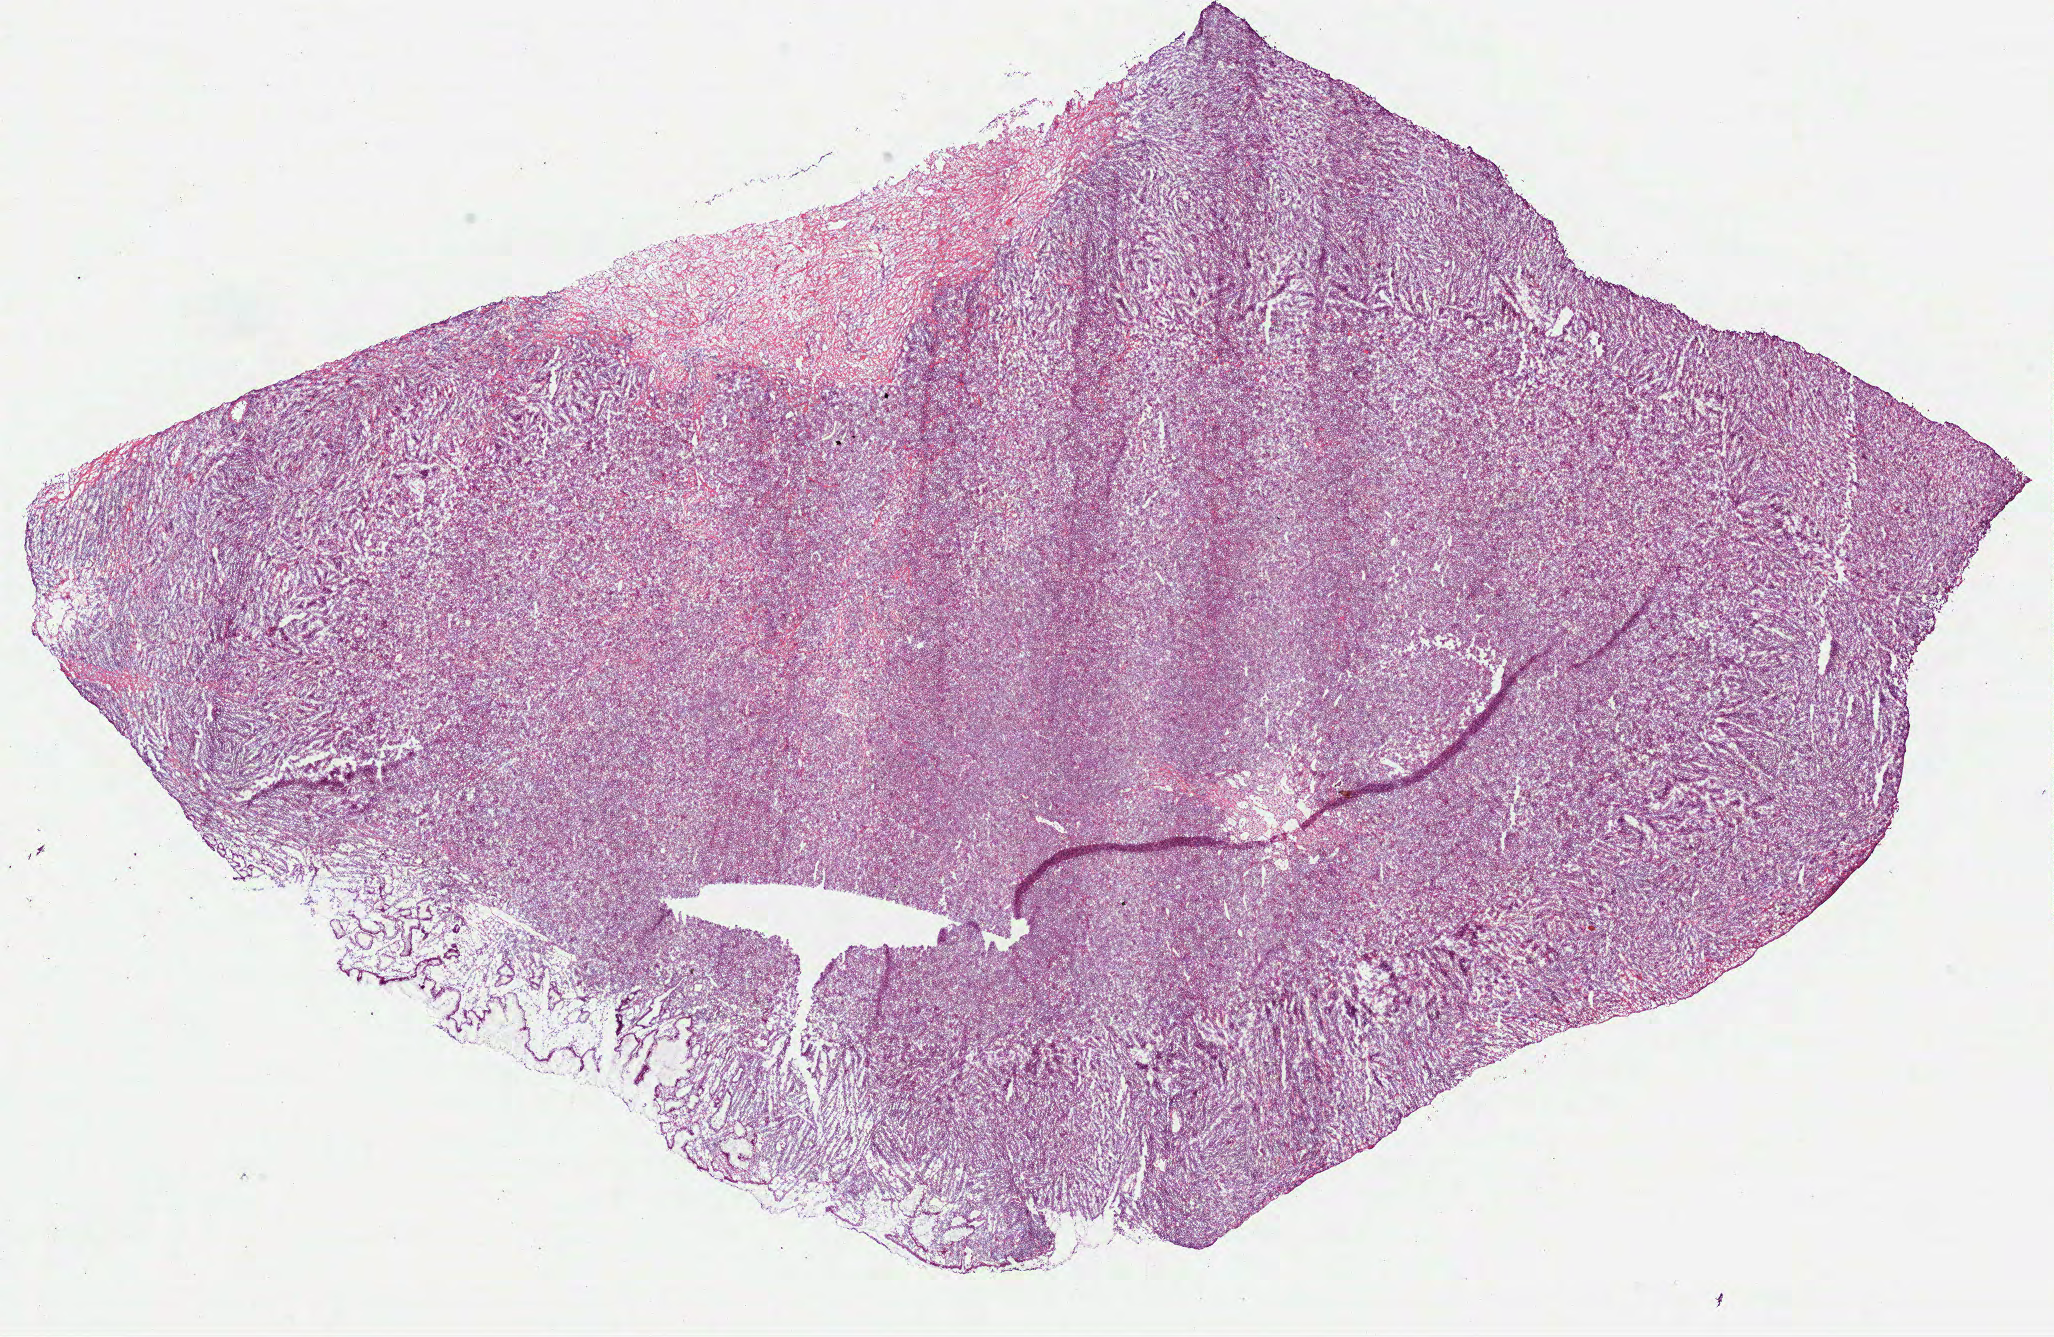
Hematoxylin and eosin (H&E) stained whole-slide image, a low-resolution overview of the entire scanned area, about 16.6 x 10.8 mm (acquisition: 40x scan), frozen section from the bottom of the tissue portion, sample: primary tumour, stomach. Female, age 66 years at initial diagnosis. Pathologist review of this section (percent, as recorded): tumour cells 87%, tumour nuclei 85%.
Diagnosis: Carcinoma, diffuse type (fundus of stomach).